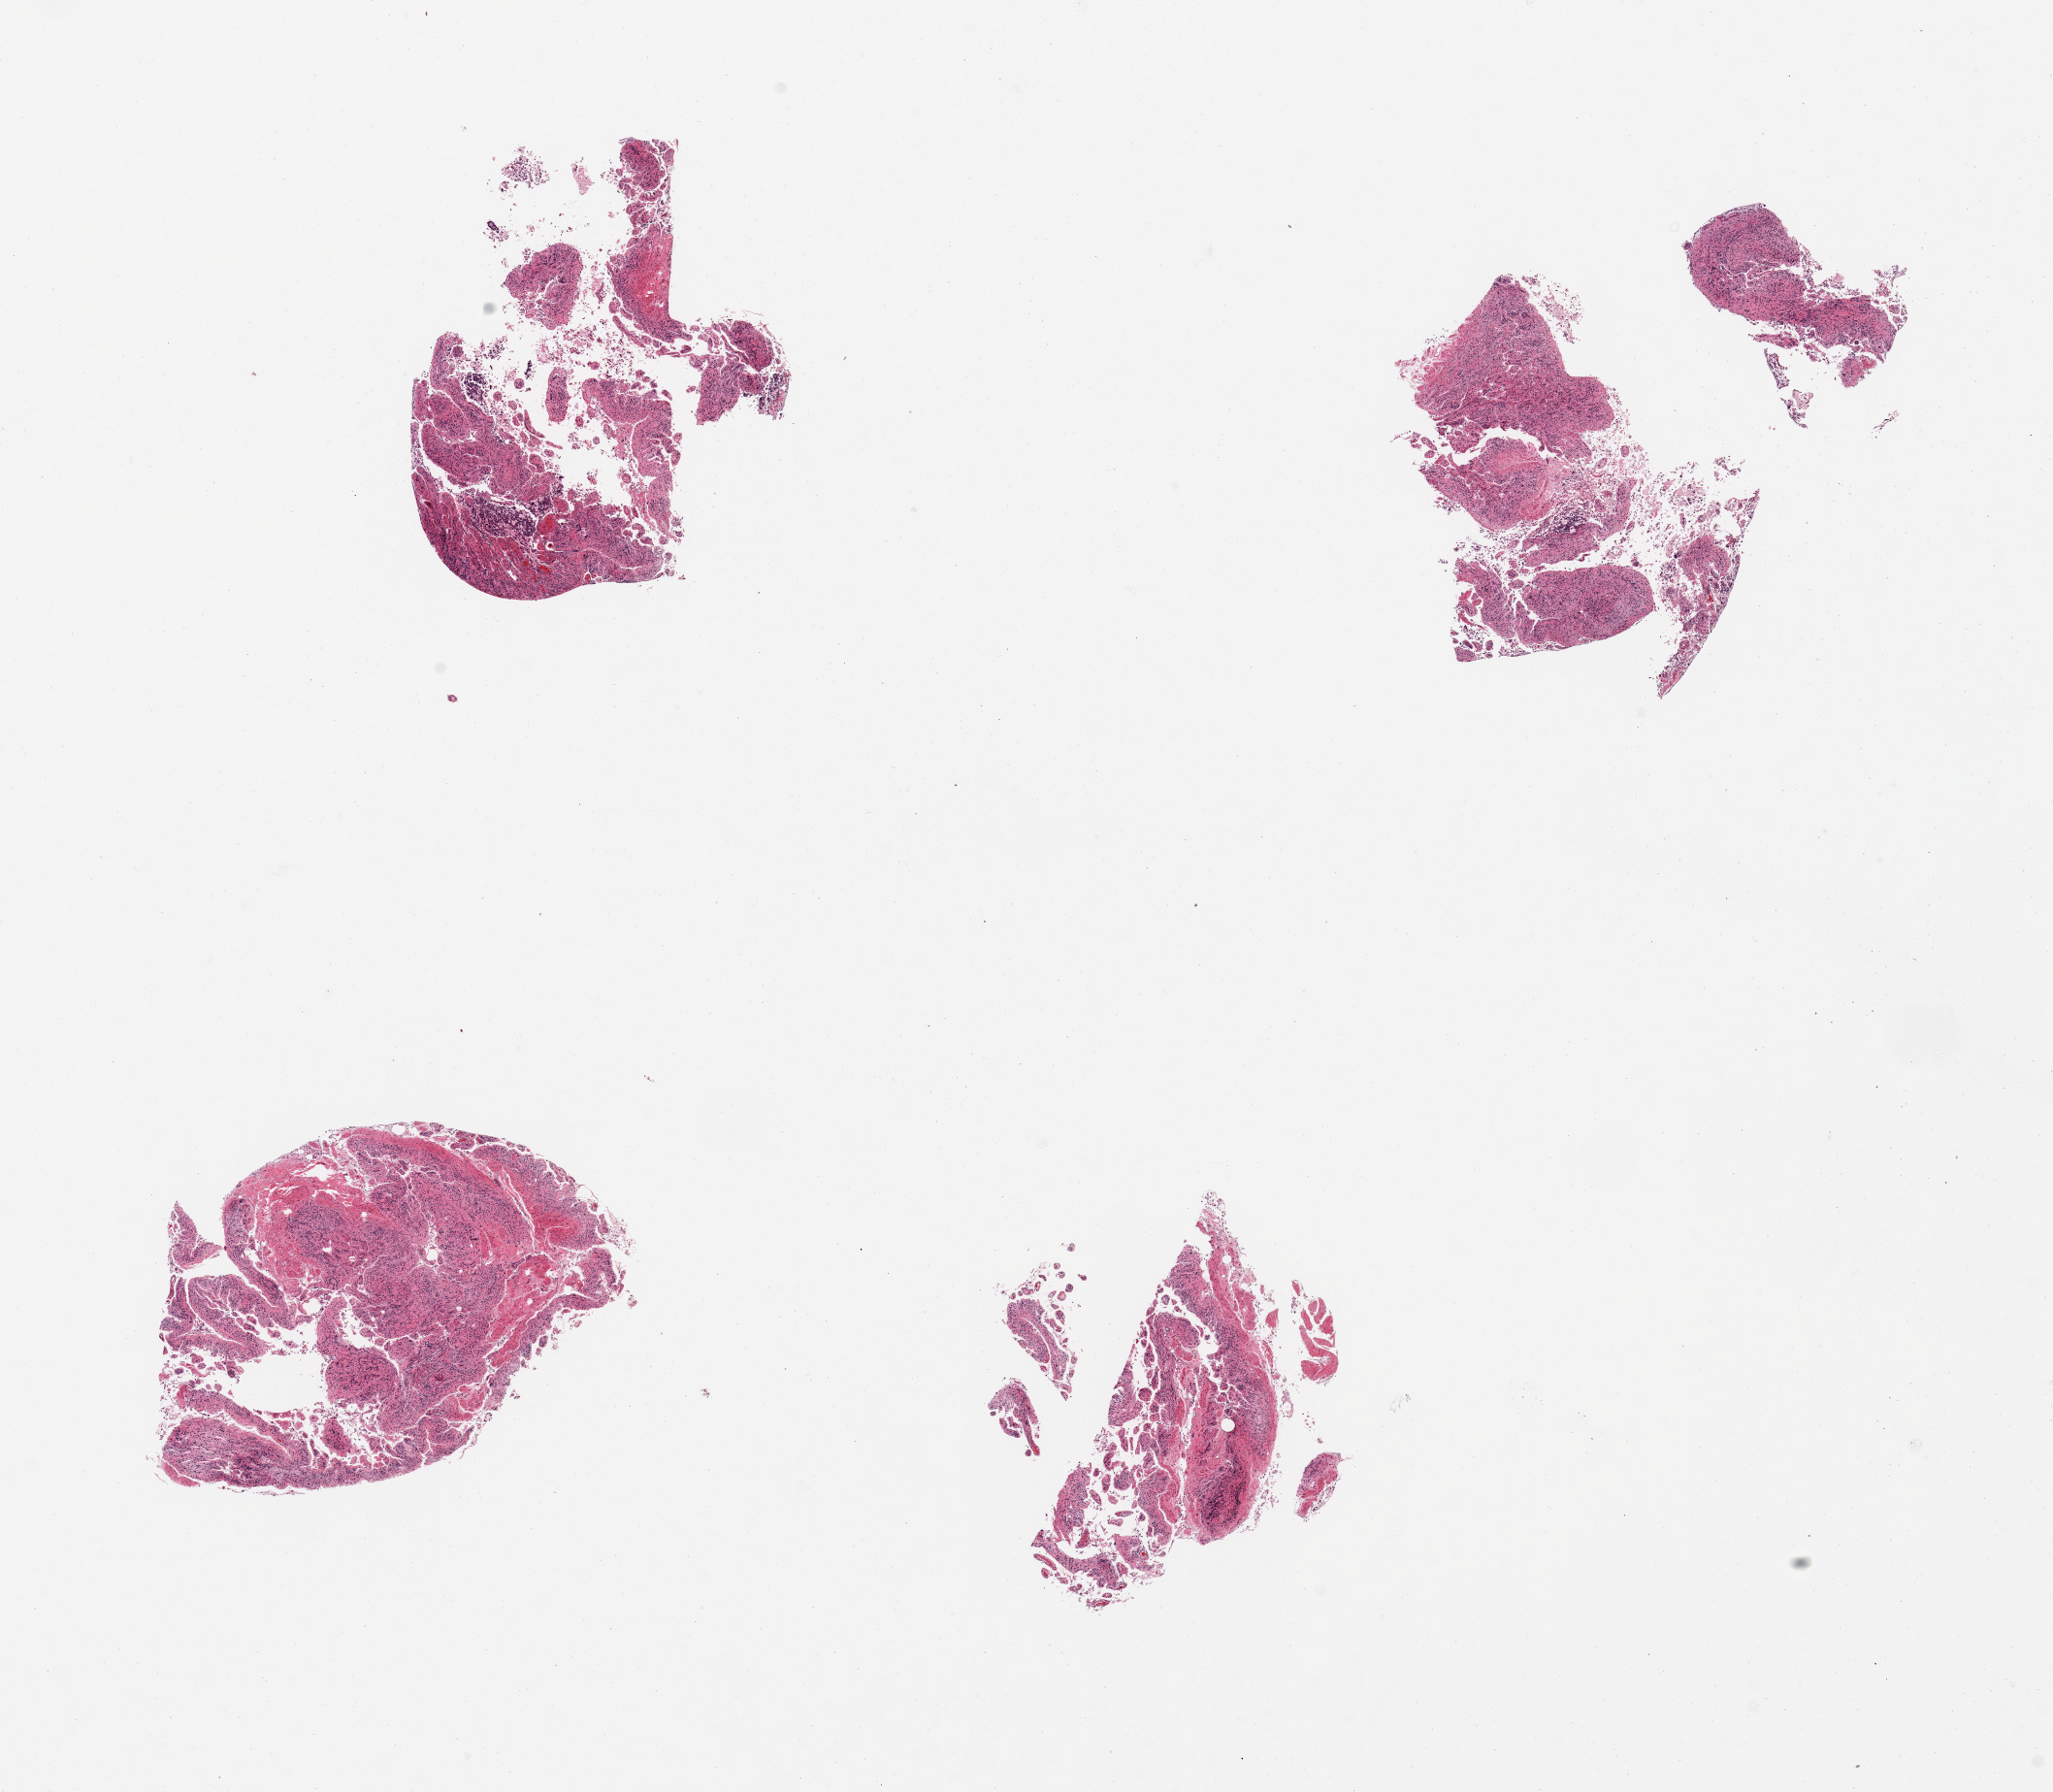
Digitized H&E-stained section — whole scanned area (about 16.7 x 14.6 mm, slide scanned at 20x) shown as a low-resolution overview. Donor sex: male.
Specimen: PAXgene-fixed paraffin-embedded (PFPE) section; target tissue: ileum; tissue donor sample.